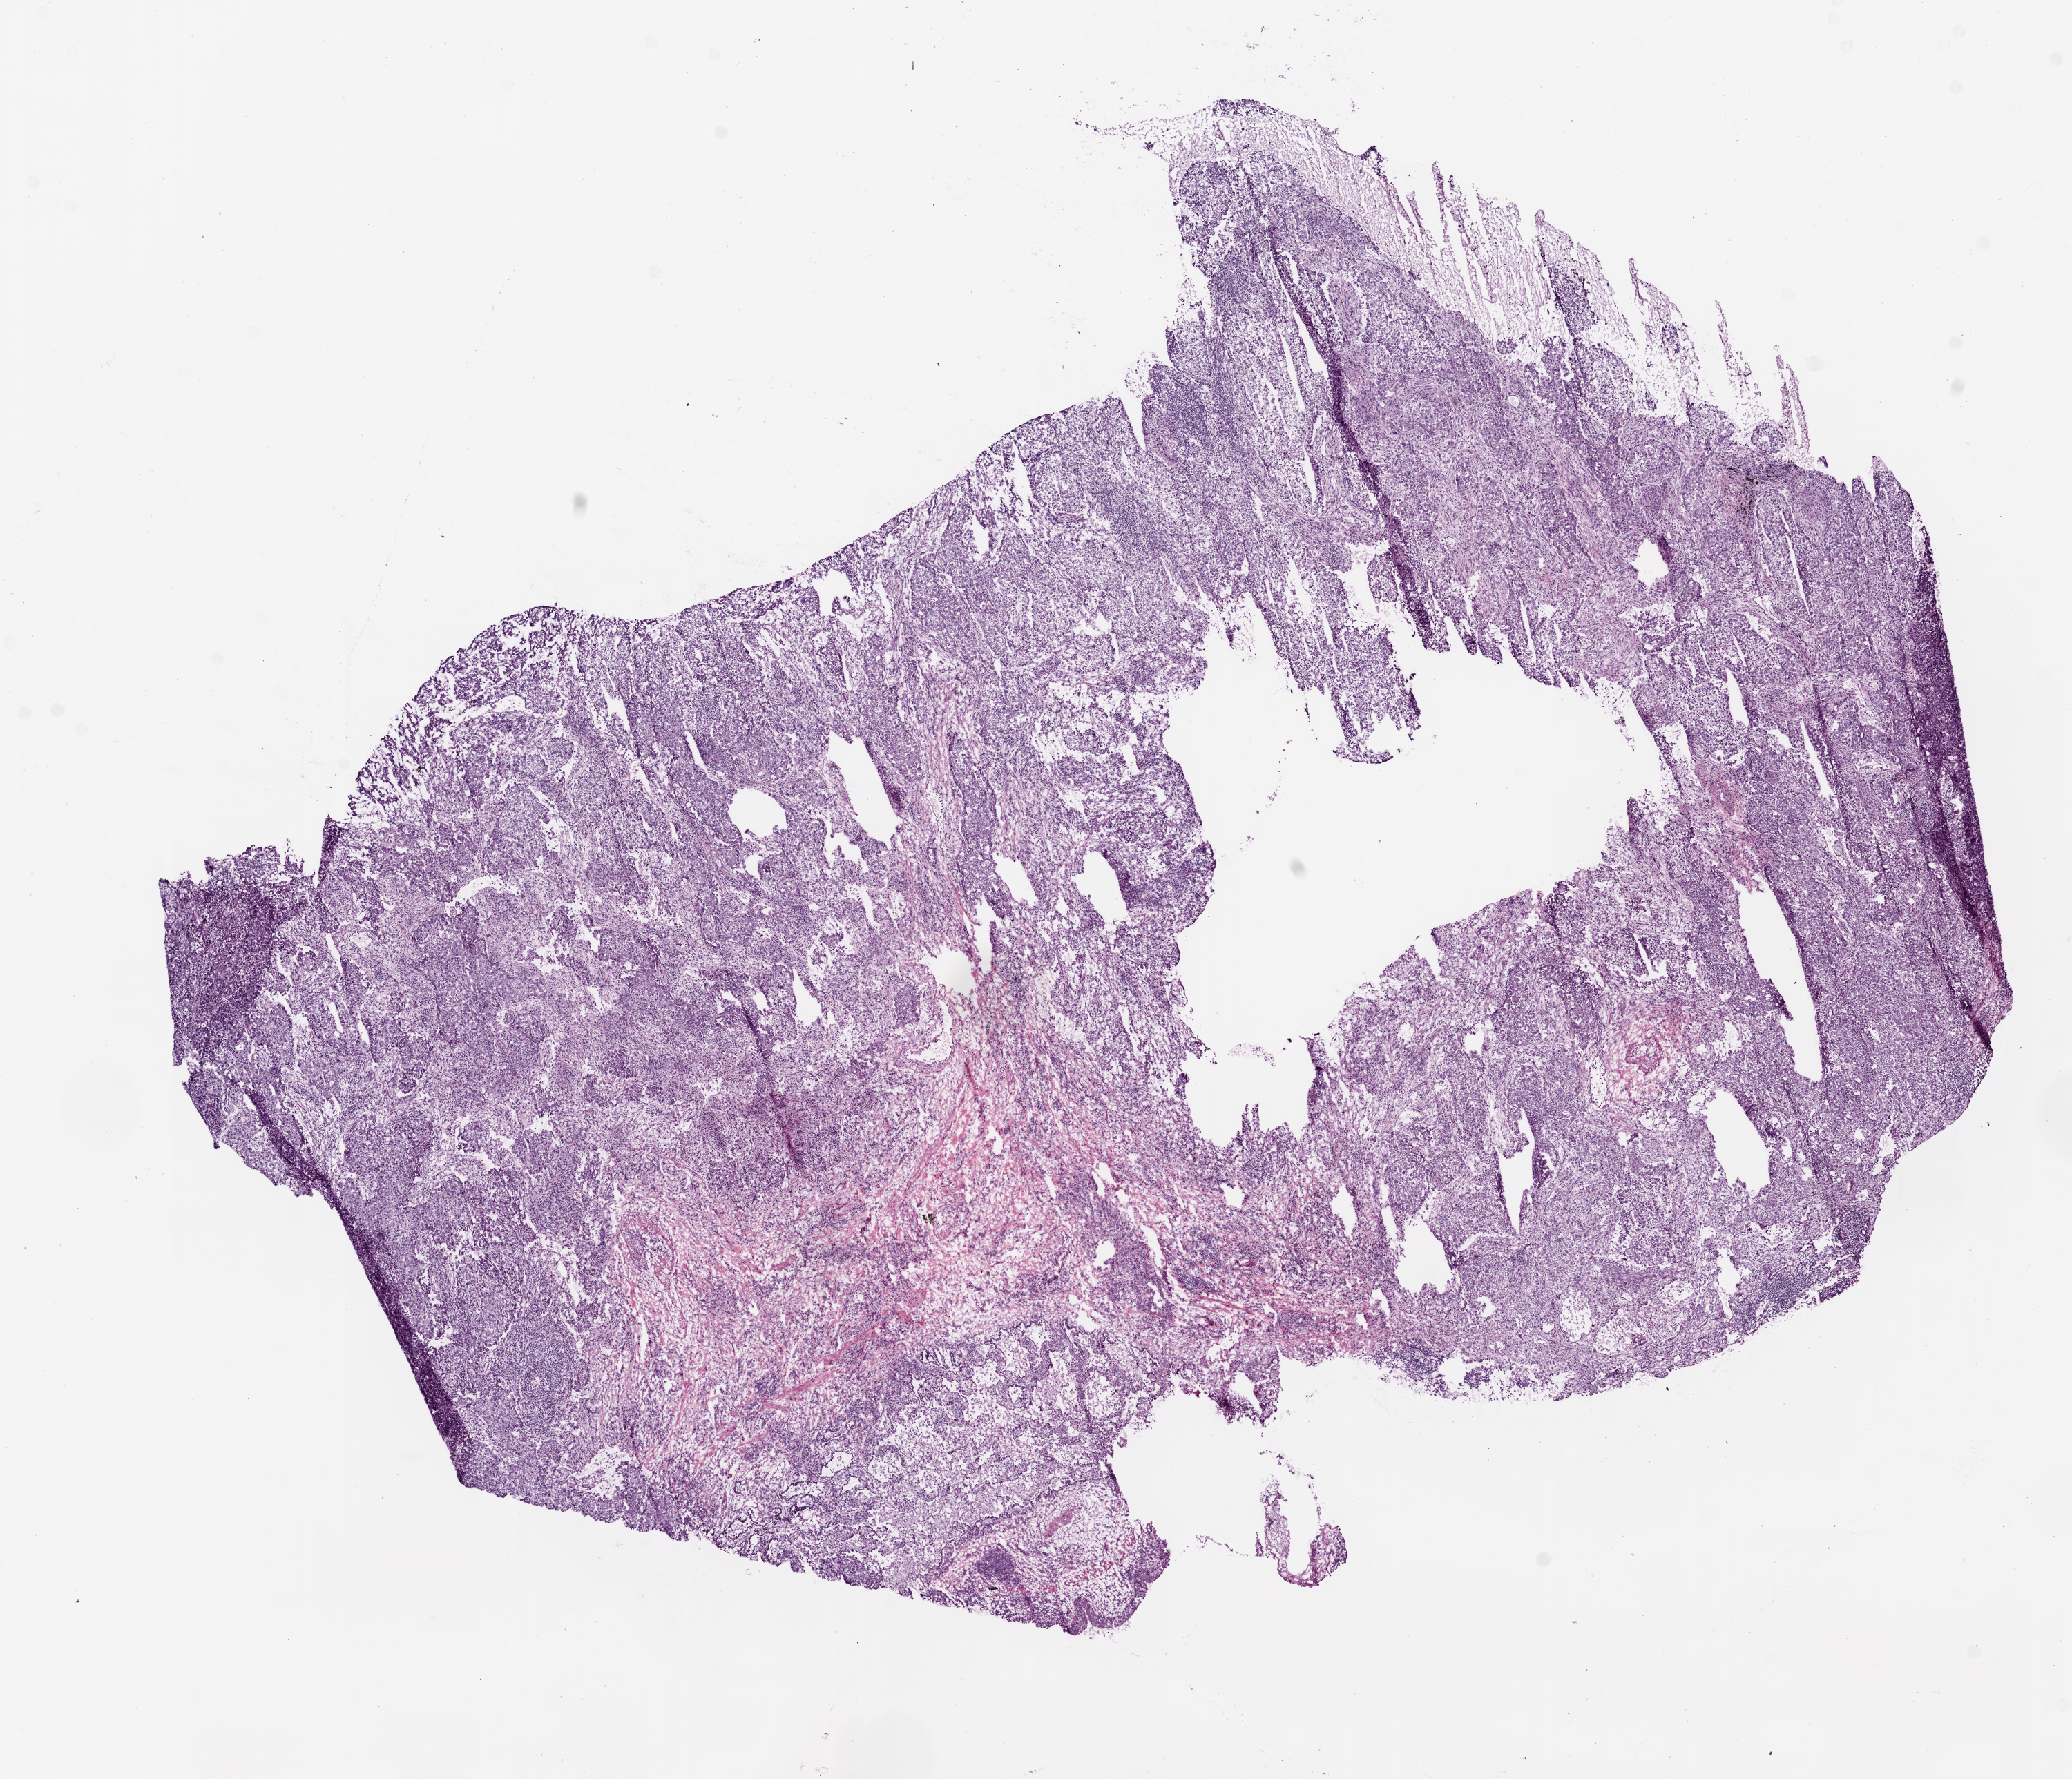
Hematoxylin and eosin (H&E) stained whole-slide image — whole scanned area (about 12.0 x 10.3 mm, acquisition: 20x scan) shown as a low-resolution overview; frozen section; lung, primary tumour sample. Female patient; age at initial diagnosis 51 years. Slide review estimates, as recorded: tumour cells 72%, tumour nuclei 70%, normal cells 15%, stromal cells 10%, necrosis 3%.
- TNM: T2 N0 M0
- AJCC pathologic stage: IB (6th edition)
- diagnosis: Adenocarcinoma with mixed subtypes